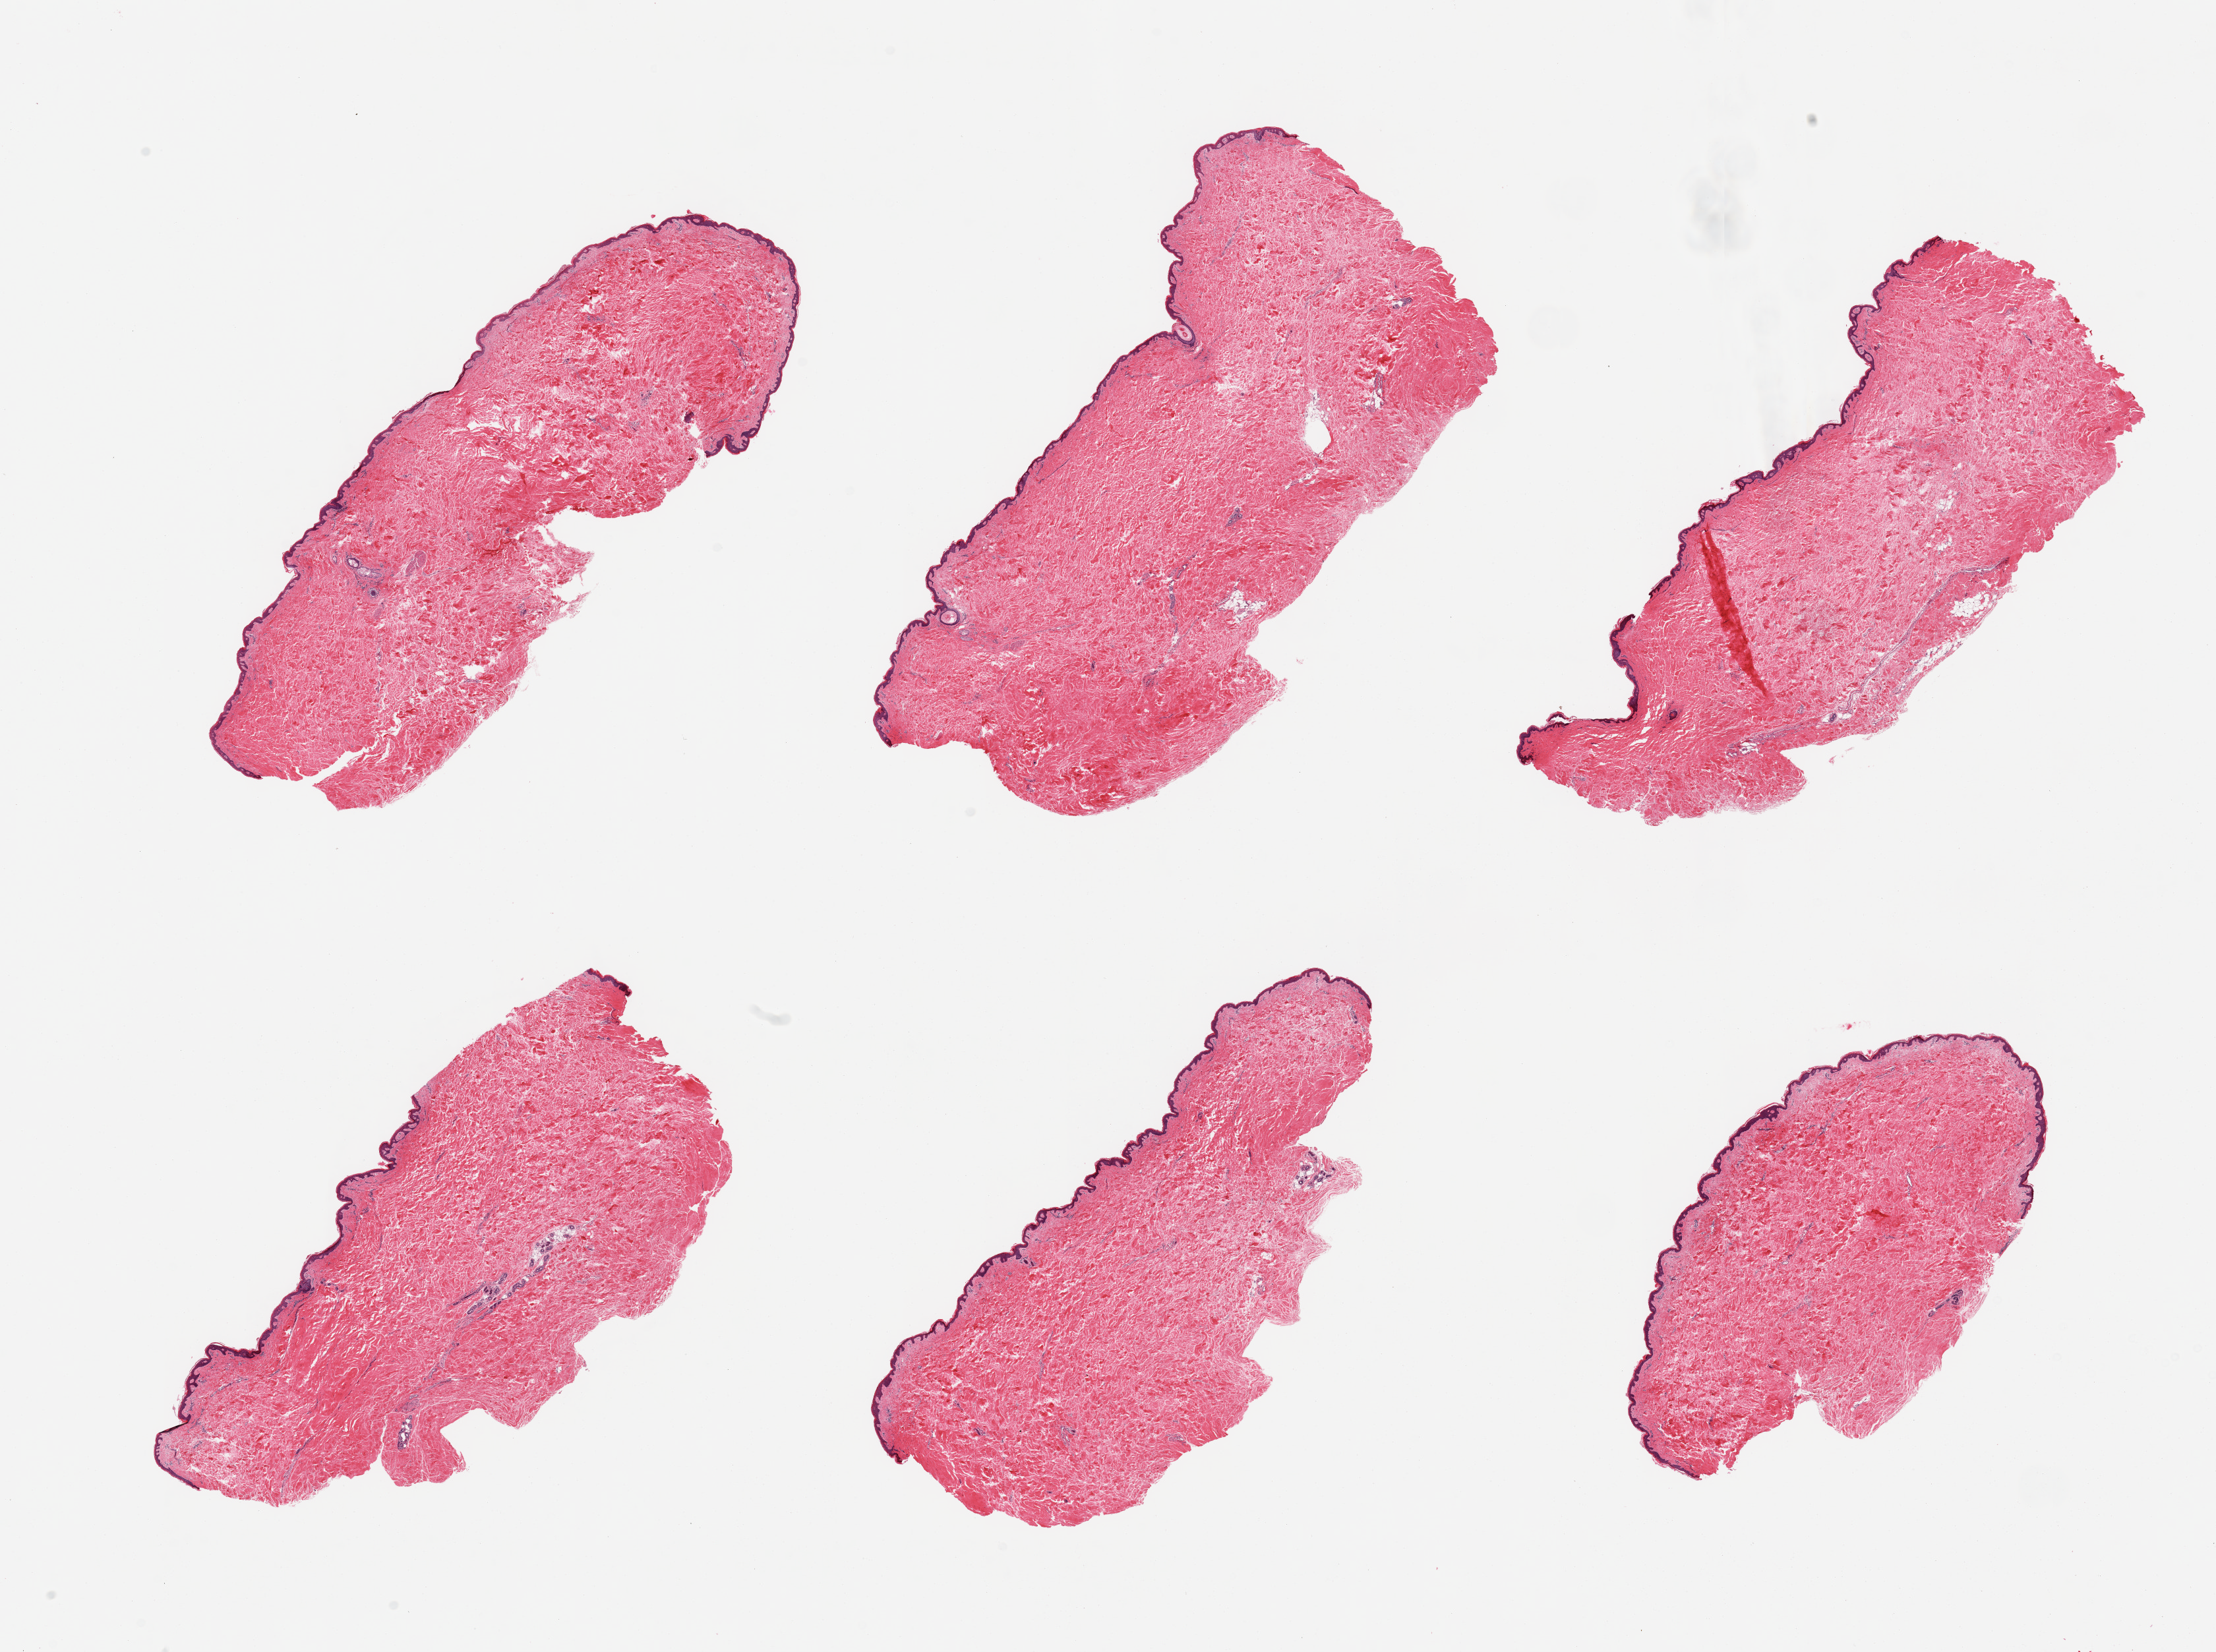
Hematoxylin and eosin (H&E) whole-slide image, brightfield, whole scanned area (about 26.6 x 19.8 mm, slide scanned at 20x) shown as a low-resolution overview; PAXgene-fixed paraffin-embedded (PFPE) section; section of skin of suprapubic region (target tissue); donor tissue sample. Donor sex: male.
- review note (as recorded): 6 pieces; 1% intradermal fat